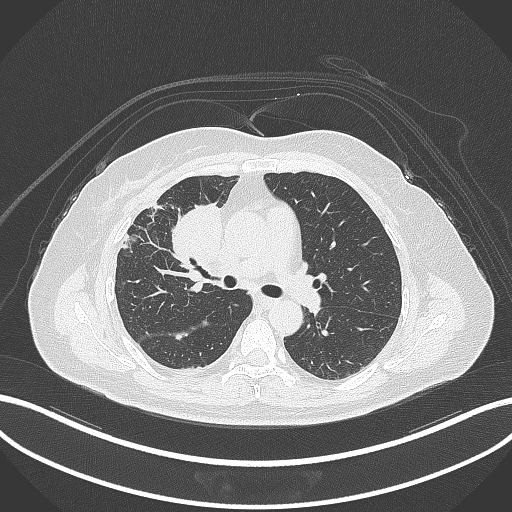
Chest CT, one axial slice. Position 168 of 305 along the scan axis. Reconstruction kernel B70f. 120 kVp. Lung window (W 1500 / L -600 HU). 1 mm slice thickness. 512 × 512 image matrix, field of view 400 × 400 mm. Female patient, age 52 years. From the clinical record (not read from this slice): clinical TNM (as recorded): T3 N1 M1.
Outlined on this slice (rectangle marked by the reading radiologist):
- lung tumour (recorded histology: adenocarcinoma): box from (x=165, y=196) to (x=226, y=280) px